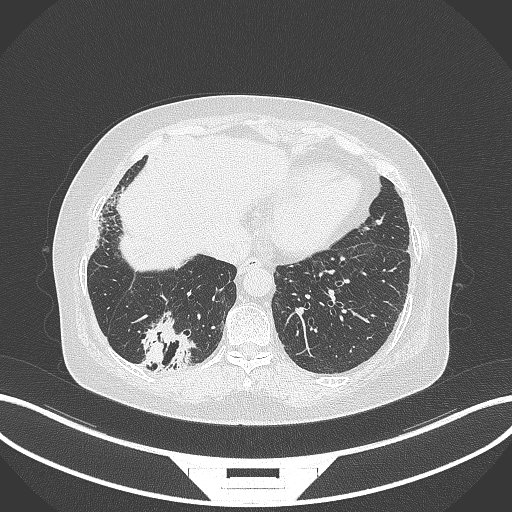
Chest CT, one axial slice. Position 49 of 296 along the scan axis. Reconstruction kernel B70f. 120 kVp. Lung window (W 1500 / L -600 HU). 1 mm slice thickness. 512 × 512 image matrix, field of view 400 × 400 mm. Patient: female, 65 years. Case-level facts recorded for this patient, not image findings: clinical TNM (as recorded): T2b N1 M0.
Annotated regions visible in this slice (bounding box drawn by a radiologist):
- lung tumour (recorded histology: adenocarcinoma): box from (x=138, y=310) to (x=195, y=373) px